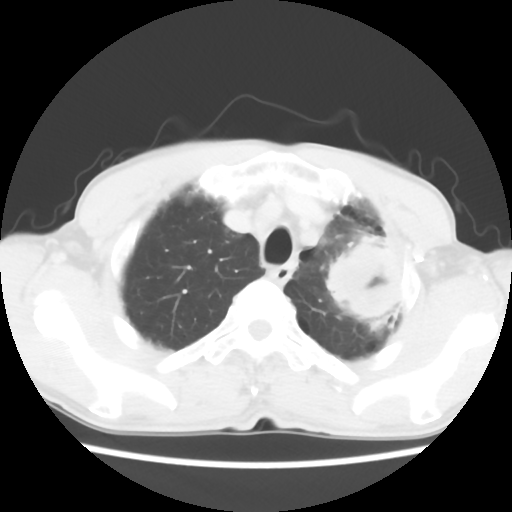
Chest CT, one axial slice; slice 50 of 60 in the series (ordered by position); 120 kVp; lung window (W 1500 / L -600 HU); 5 mm slice thickness; 512 × 512 image matrix. Male patient, age 64 years. Case-level facts recorded for this patient, not image findings: clinical TNM (as recorded): T3 N3 M0; histopathological grade: G3.
Outlined on this slice (bounding box drawn by a radiologist):
- lung tumour (recorded histology: adenocarcinoma): box from (x=319, y=232) to (x=408, y=334) px